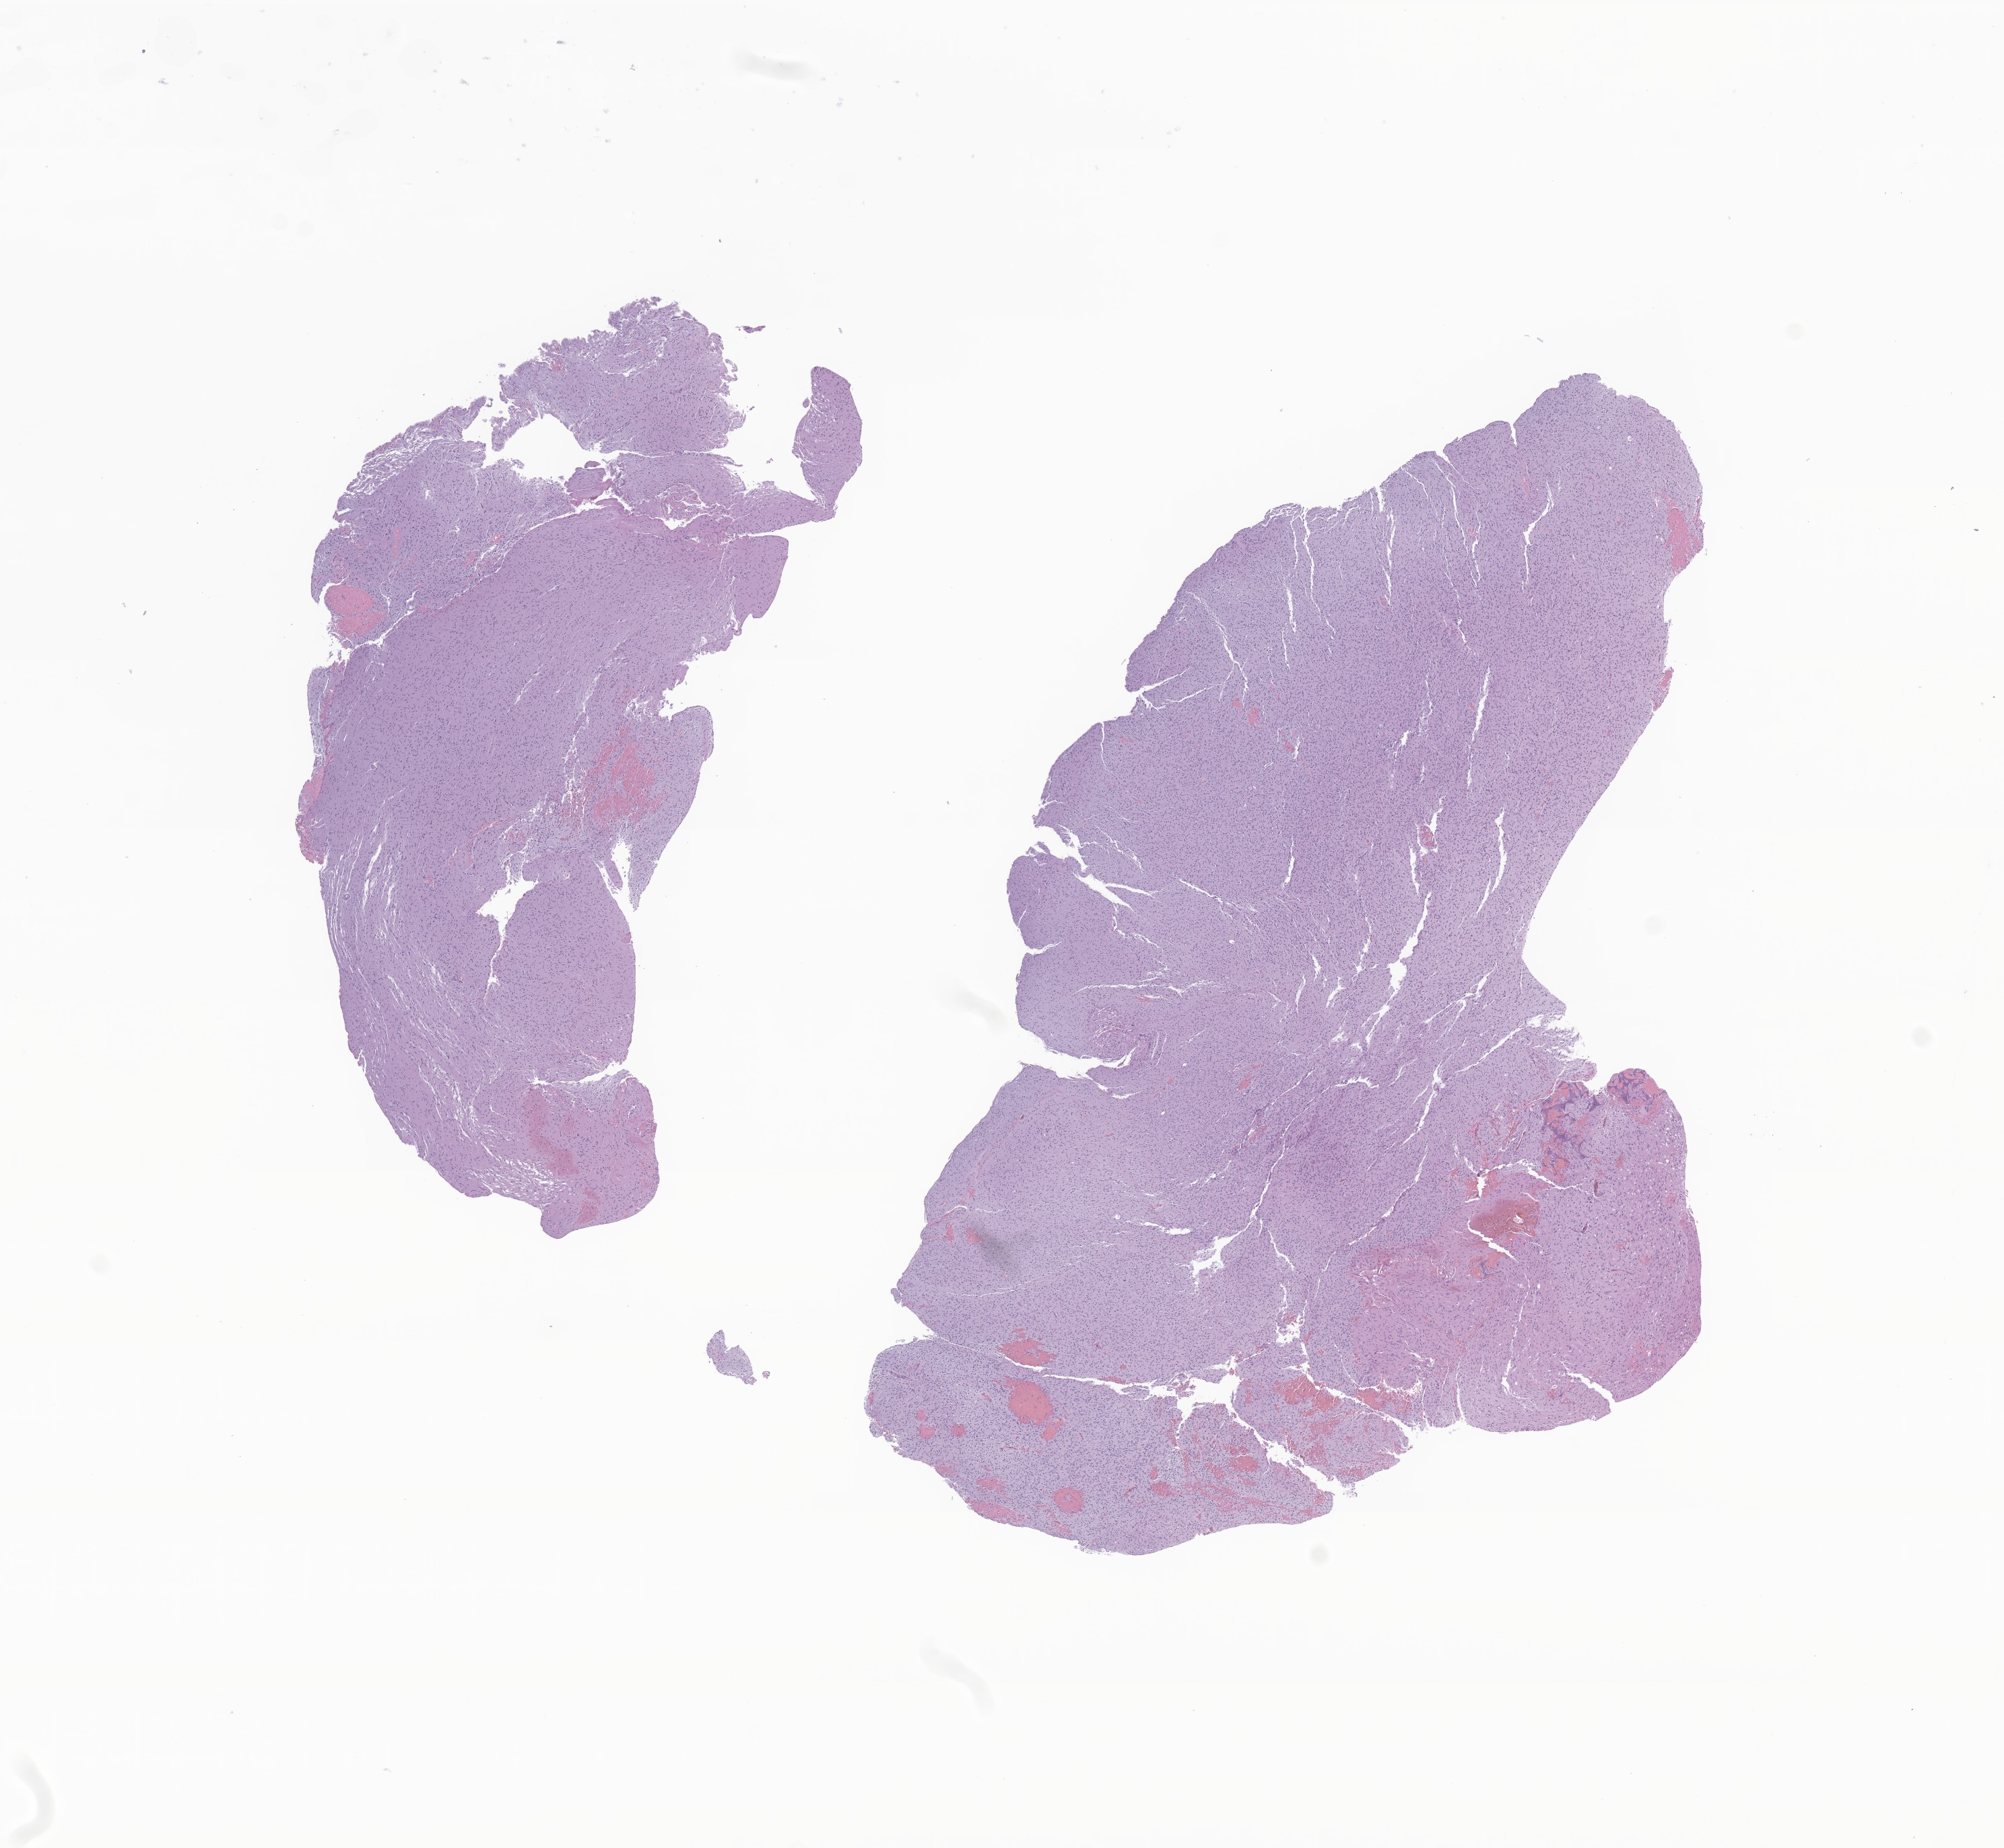
H&E whole-slide image of tumor tissue from the spinal cord, shown as a low-resolution overview of the whole scanned area (about 12.5 x 11.6 mm); FFPE section. Patient male; age 170 months (14 years 2 months).
Diagnosis: Glioma, malignant.